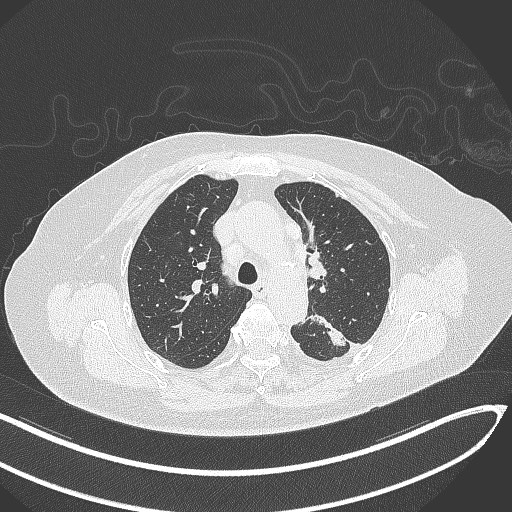
Chest CT, one axial slice. Position 222 of 270 along the scan axis. Reconstruction kernel B70f. Lung window (W 1500 / L -600 HU). 1 mm slice thickness. 512 × 512 image matrix. Patient: female, 76 years. From the clinical record (not read from this slice): clinical TNM (as recorded): T1c N0 M0.
Outlined on this slice (rectangle marked by the reading radiologist):
- lung tumour (recorded histology: adenocarcinoma): bounding box [x1, y1, x2, y2] px = [308, 311, 354, 353]